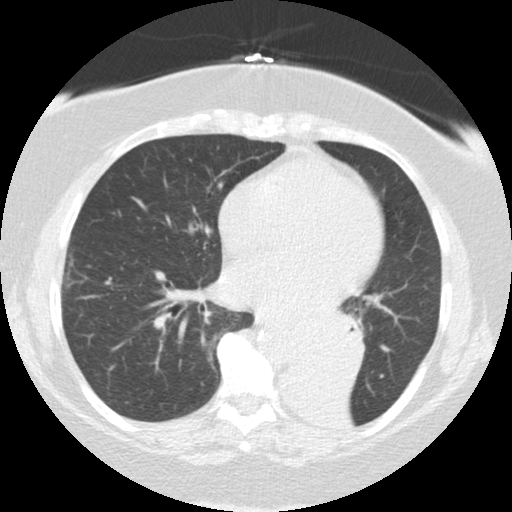
Low-dose screening chest CT, axial slice, baseline screening round, lung window (W 1500 / L -600 HU), 512 × 512 image matrix. Female, age 71 years at enrolment. Former smoker at enrolment.
Expert-annotated lung lesion, bounding box <282,304,368,384> (left, top, right, bottom; pixels). Reader record for this screening exam (exam-level; its link to the box is not recorded): non-calcified nodule or mass ≥4 mm, right middle lobe, 5 × 5 mm, smooth margins, soft tissue attenuation. Note: the box lies in the patient's left hemithorax on this image, whereas the reader's record names the right lung; they may be different findings. Participant outcome: lung cancer diagnosed 46 days after this screen — large cell carcinoma, NOS, left lower lobe, mediastinum, other location, poorly differentiated (G3), stage IV (AJCC 6th edition), 50 mm at pathology.